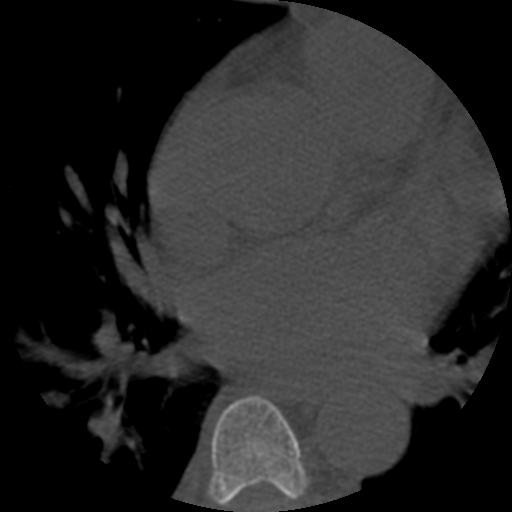
CT including the spine, one axial slice. Slice 352 of 508 in the series (ordered by position). 120 kVp. Bone window (W 1800 / L 400 HU). 1.25 mm slice thickness. 512 × 512 image matrix, field of view 160 × 160 mm. Patient age 57 years. From the clinical record (not read from this slice): primary cancer: prostate.
Structures marked on this image (semi-automatic segmentation, software-assisted and operator-edited):
- T6 vertebra: box from (x=209, y=396) to (x=308, y=507) px